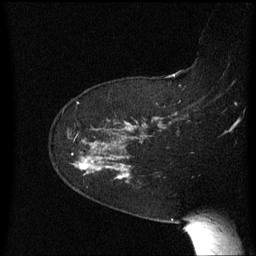
Breast MRI (dynamic contrast-enhanced), one sagittal slice; position 44 of 60 along the scan axis; dynamic contrast-enhanced series, image 2 of 3 at this slice position (ordered by acquisition); 1.5 T; TE 4.2 ms, TR 8.4 ms; 256 × 256 image matrix, field of view 200 × 200 mm. Patient: female, 63 years. From the clinical record (not read from this slice): setting: breast cancer imaged before/during neoadjuvant chemotherapy; receptor status: HER2-positive.
Structures marked on this image (semi-automatic segmentation, software-assisted and operator-edited):
- analysis volume of interest (the breast-tissue region the enhancement analysis was run in; not a lesion): box from (x=69, y=136) to (x=138, y=189) px
- tumour enhancement mask (voxels above the 70 % enhancement threshold inside the analysis volume of interest): (x=81, y=162)–(x=123, y=179)